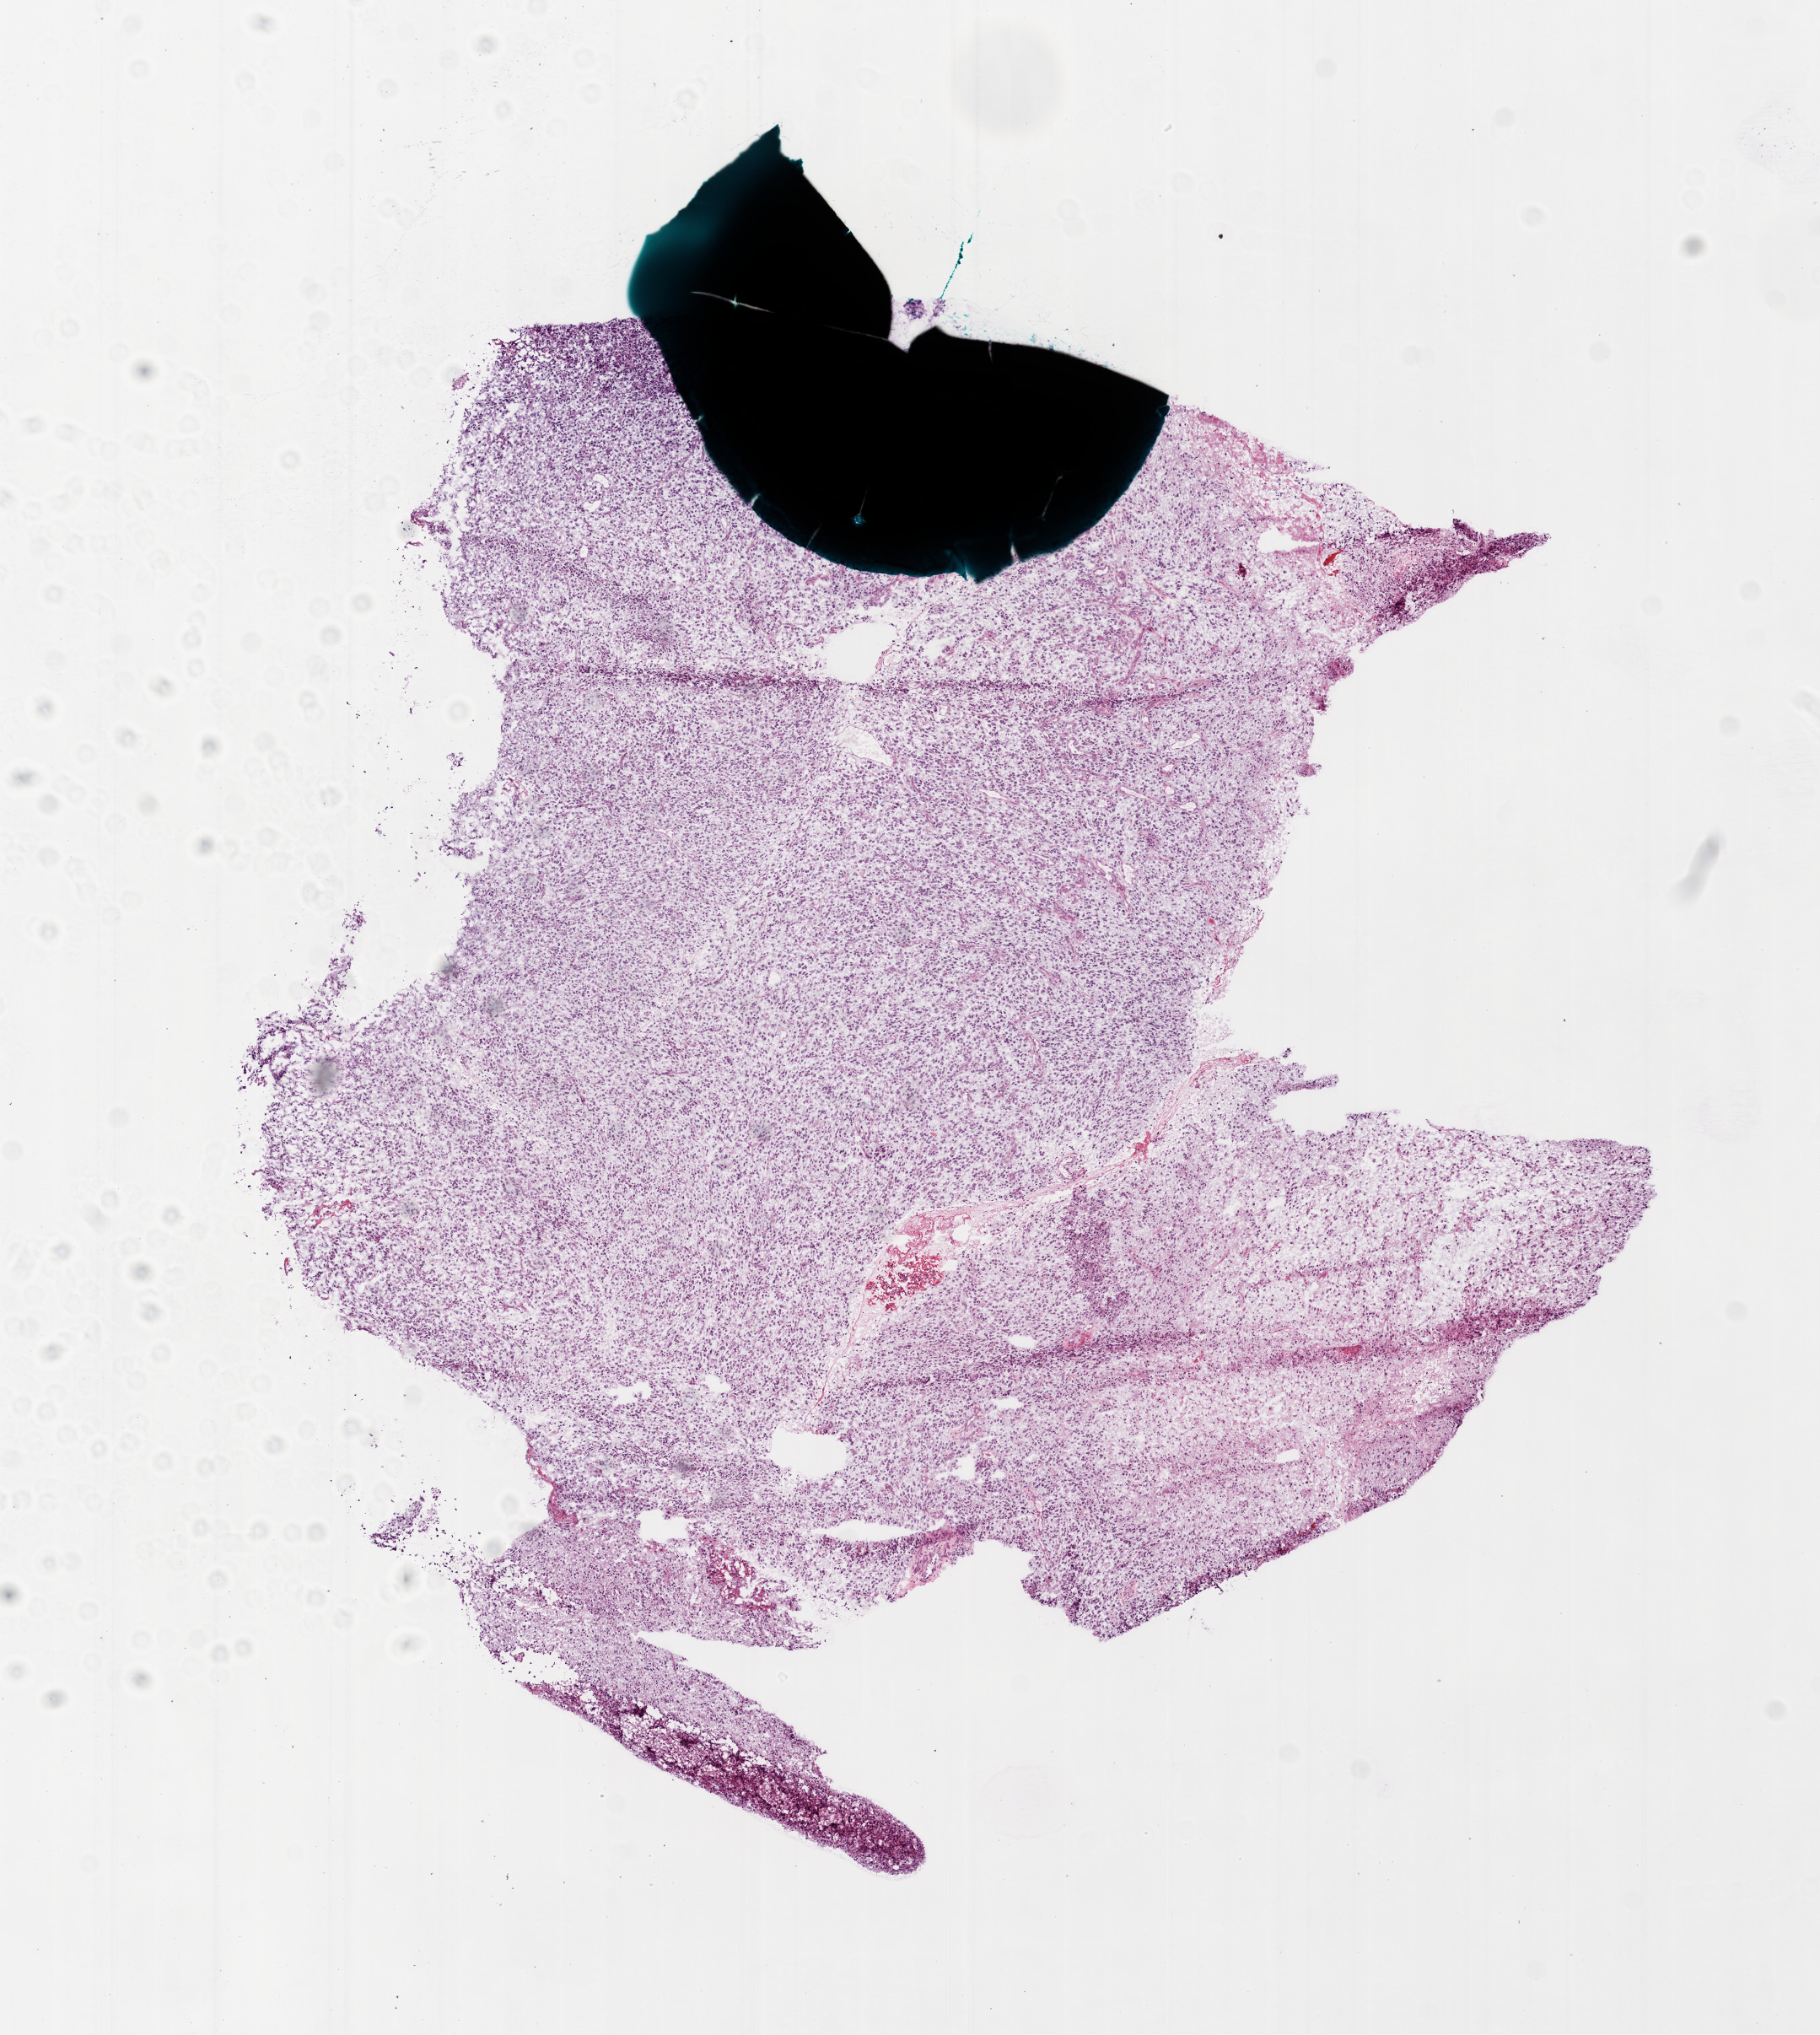
Whole-slide histology image, H&E, shown as a low-resolution overview of the whole scanned area (about 8.7 x 9.7 mm, slide scanned at 20x). Frozen section. Sample: primary tumour, brain. Patient: male, age at initial diagnosis 66 years. Composition of this section per pathologist review: tumour cells 90%, tumour nuclei 100%, normal cells 0%, stromal cells 0%, necrosis 10%.
Pathologic diagnosis: Glioblastoma.